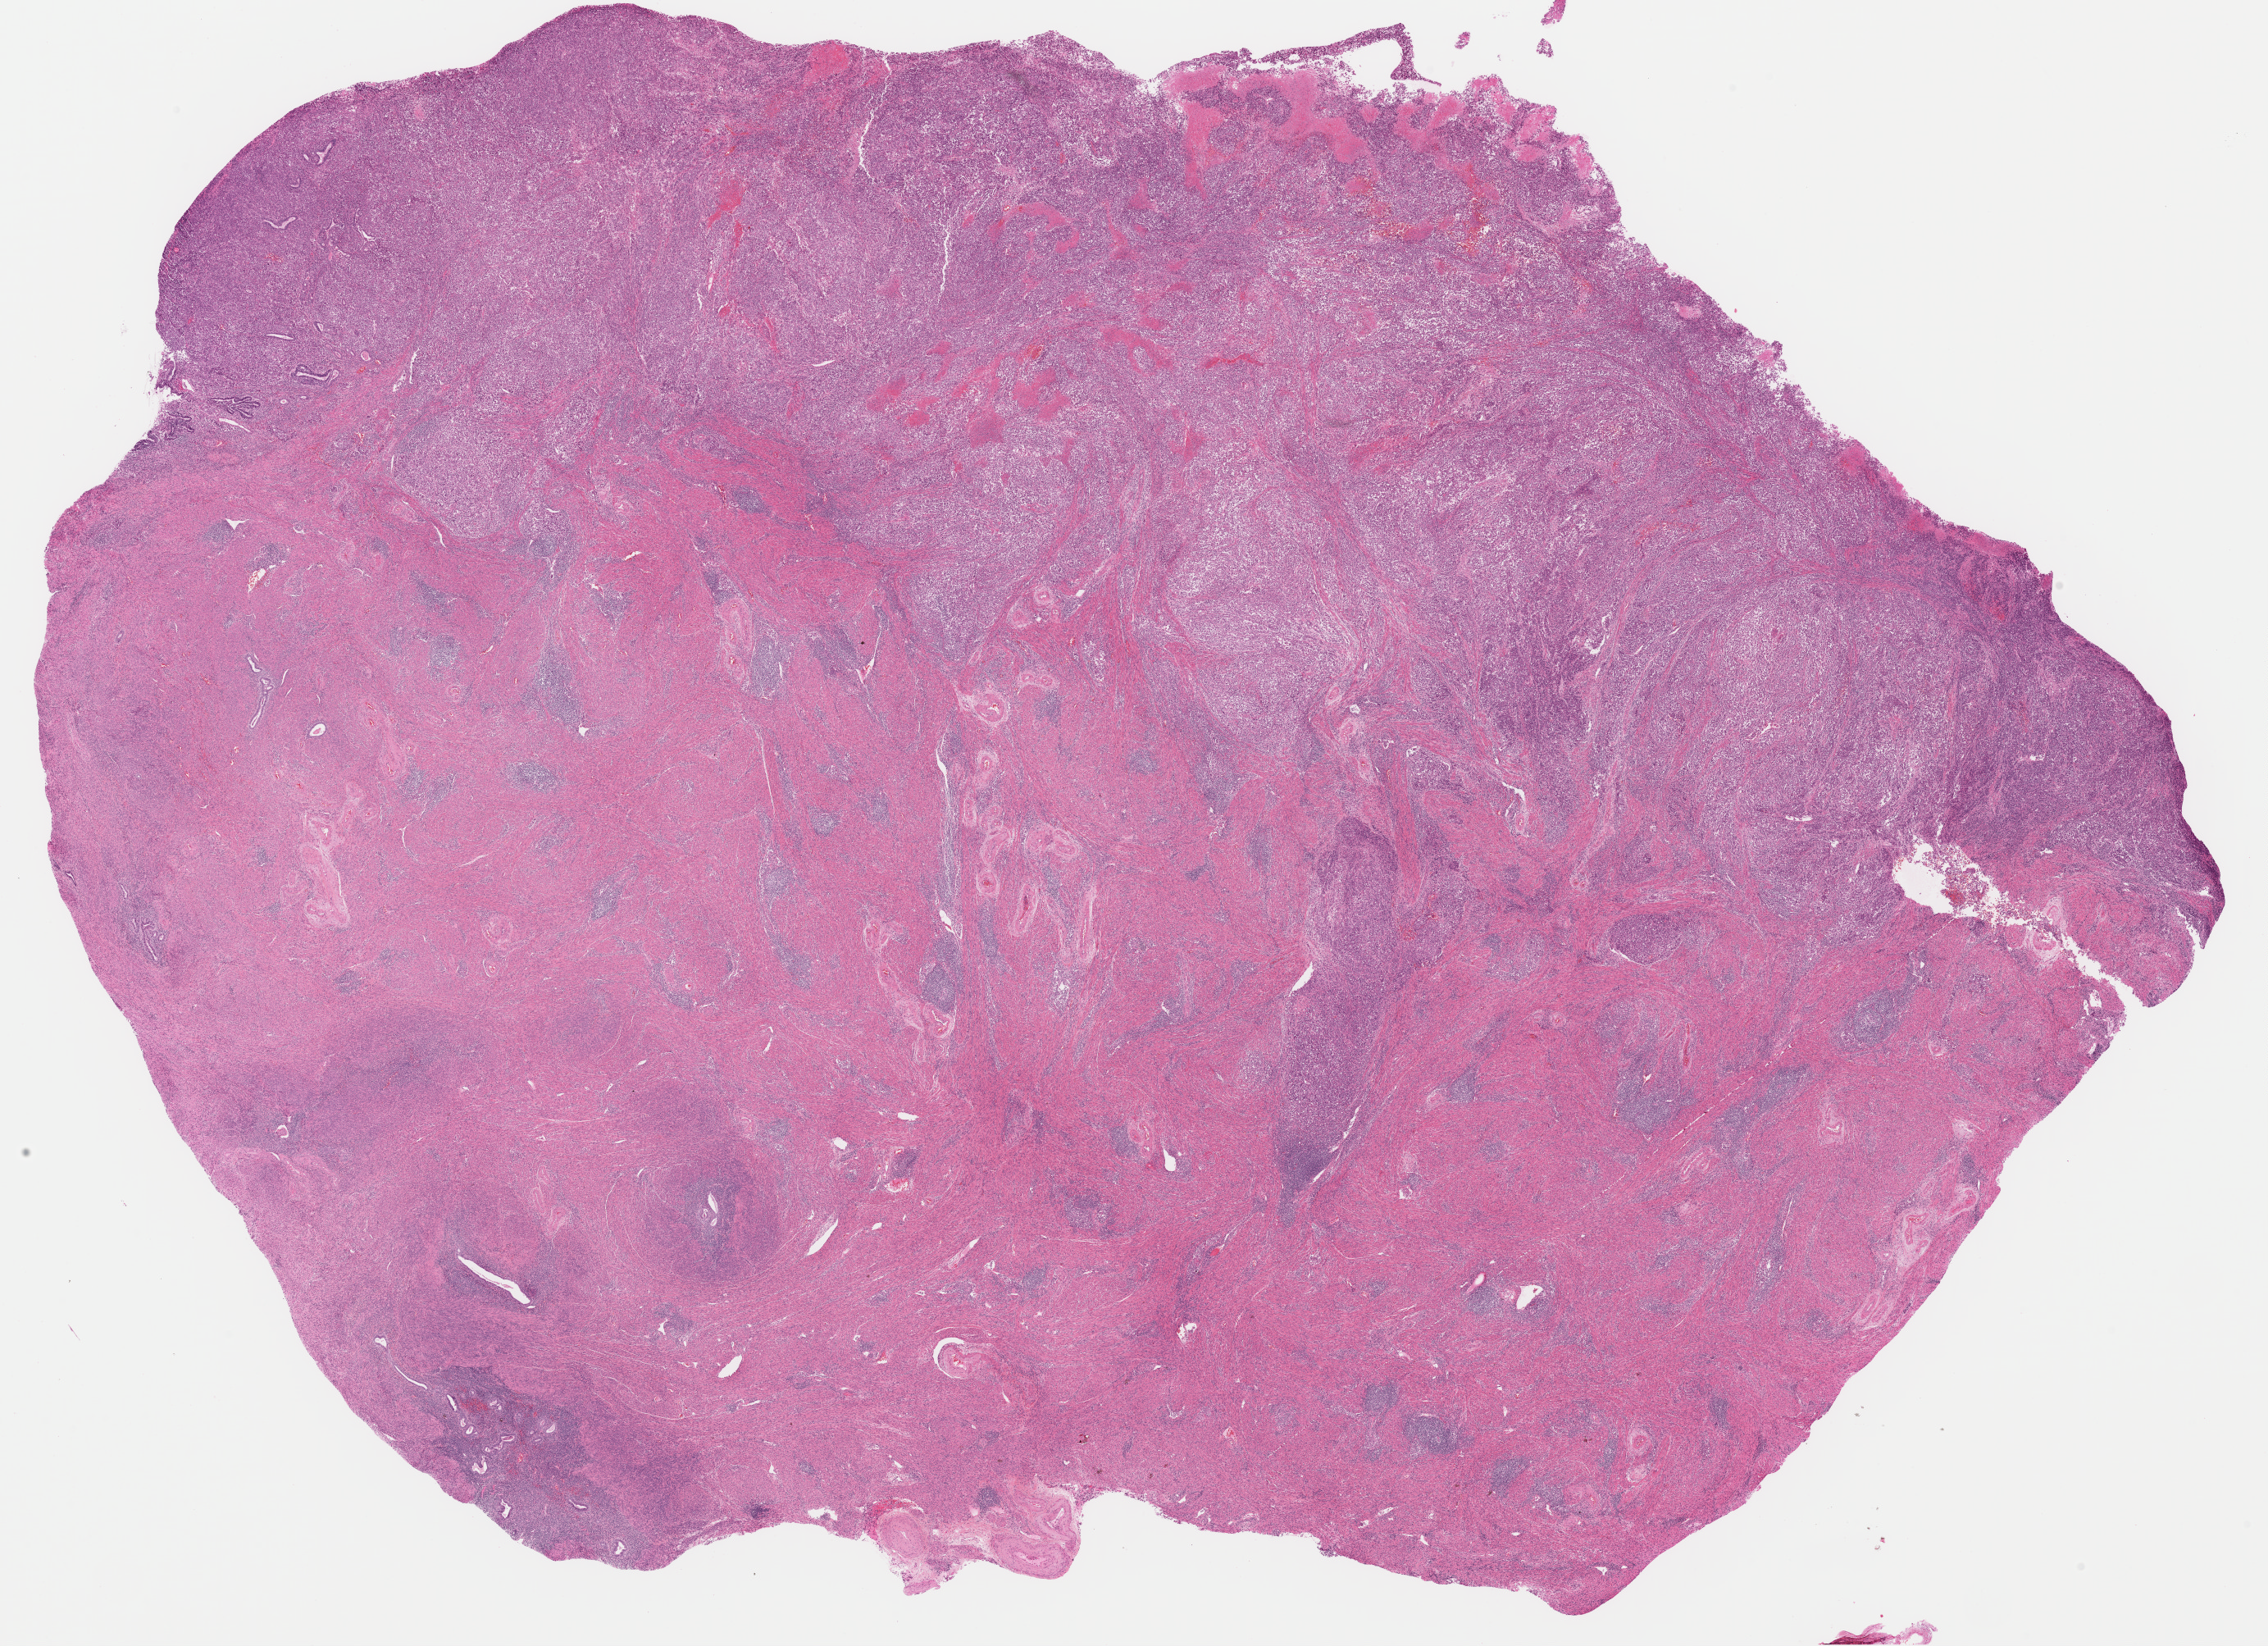
Whole-slide histology image, H&E — a low-resolution overview of the entire scanned area, about 21.9 x 15.9 mm (from a 40x scan), formalin-fixed paraffin-embedded (FFPE) diagnostic section, primary tumour sample from the uterus. Patient: female, age at initial diagnosis 68 years. Histologic grade: G3 (poorly differentiated).
FIGO stage: IA. Diagnosis: Serous cystadenocarcinoma, NOS.